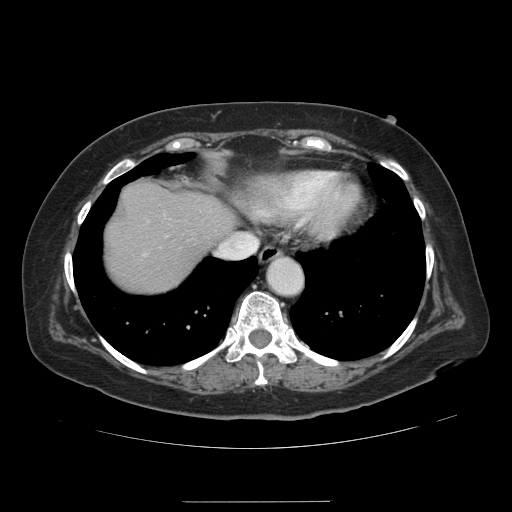
Contrast-enhanced abdominal CT, one axial slice; position 121 of 141 along the scan axis; 120 kVp; intravenous contrast given; soft-tissue window (W 400 / L 40 HU); 512 × 512 image matrix. Female patient, age 74 years. Case-level facts recorded for this patient, not image findings: diagnosis: colorectal cancer liver metastases, imaged before liver resection; multiple liver metastases: yes; largest metastasis: 7 cm; disease in both lobes: yes.
Structures marked on this image (manually delineated by an expert):
- hepatic veins: bounding box [x1, y1, x2, y2] px = [226, 233, 246, 246]
- liver: [106, 185, 236, 292]
- planned liver remnant (the part of the liver to remain after resection): [106, 185, 236, 291]